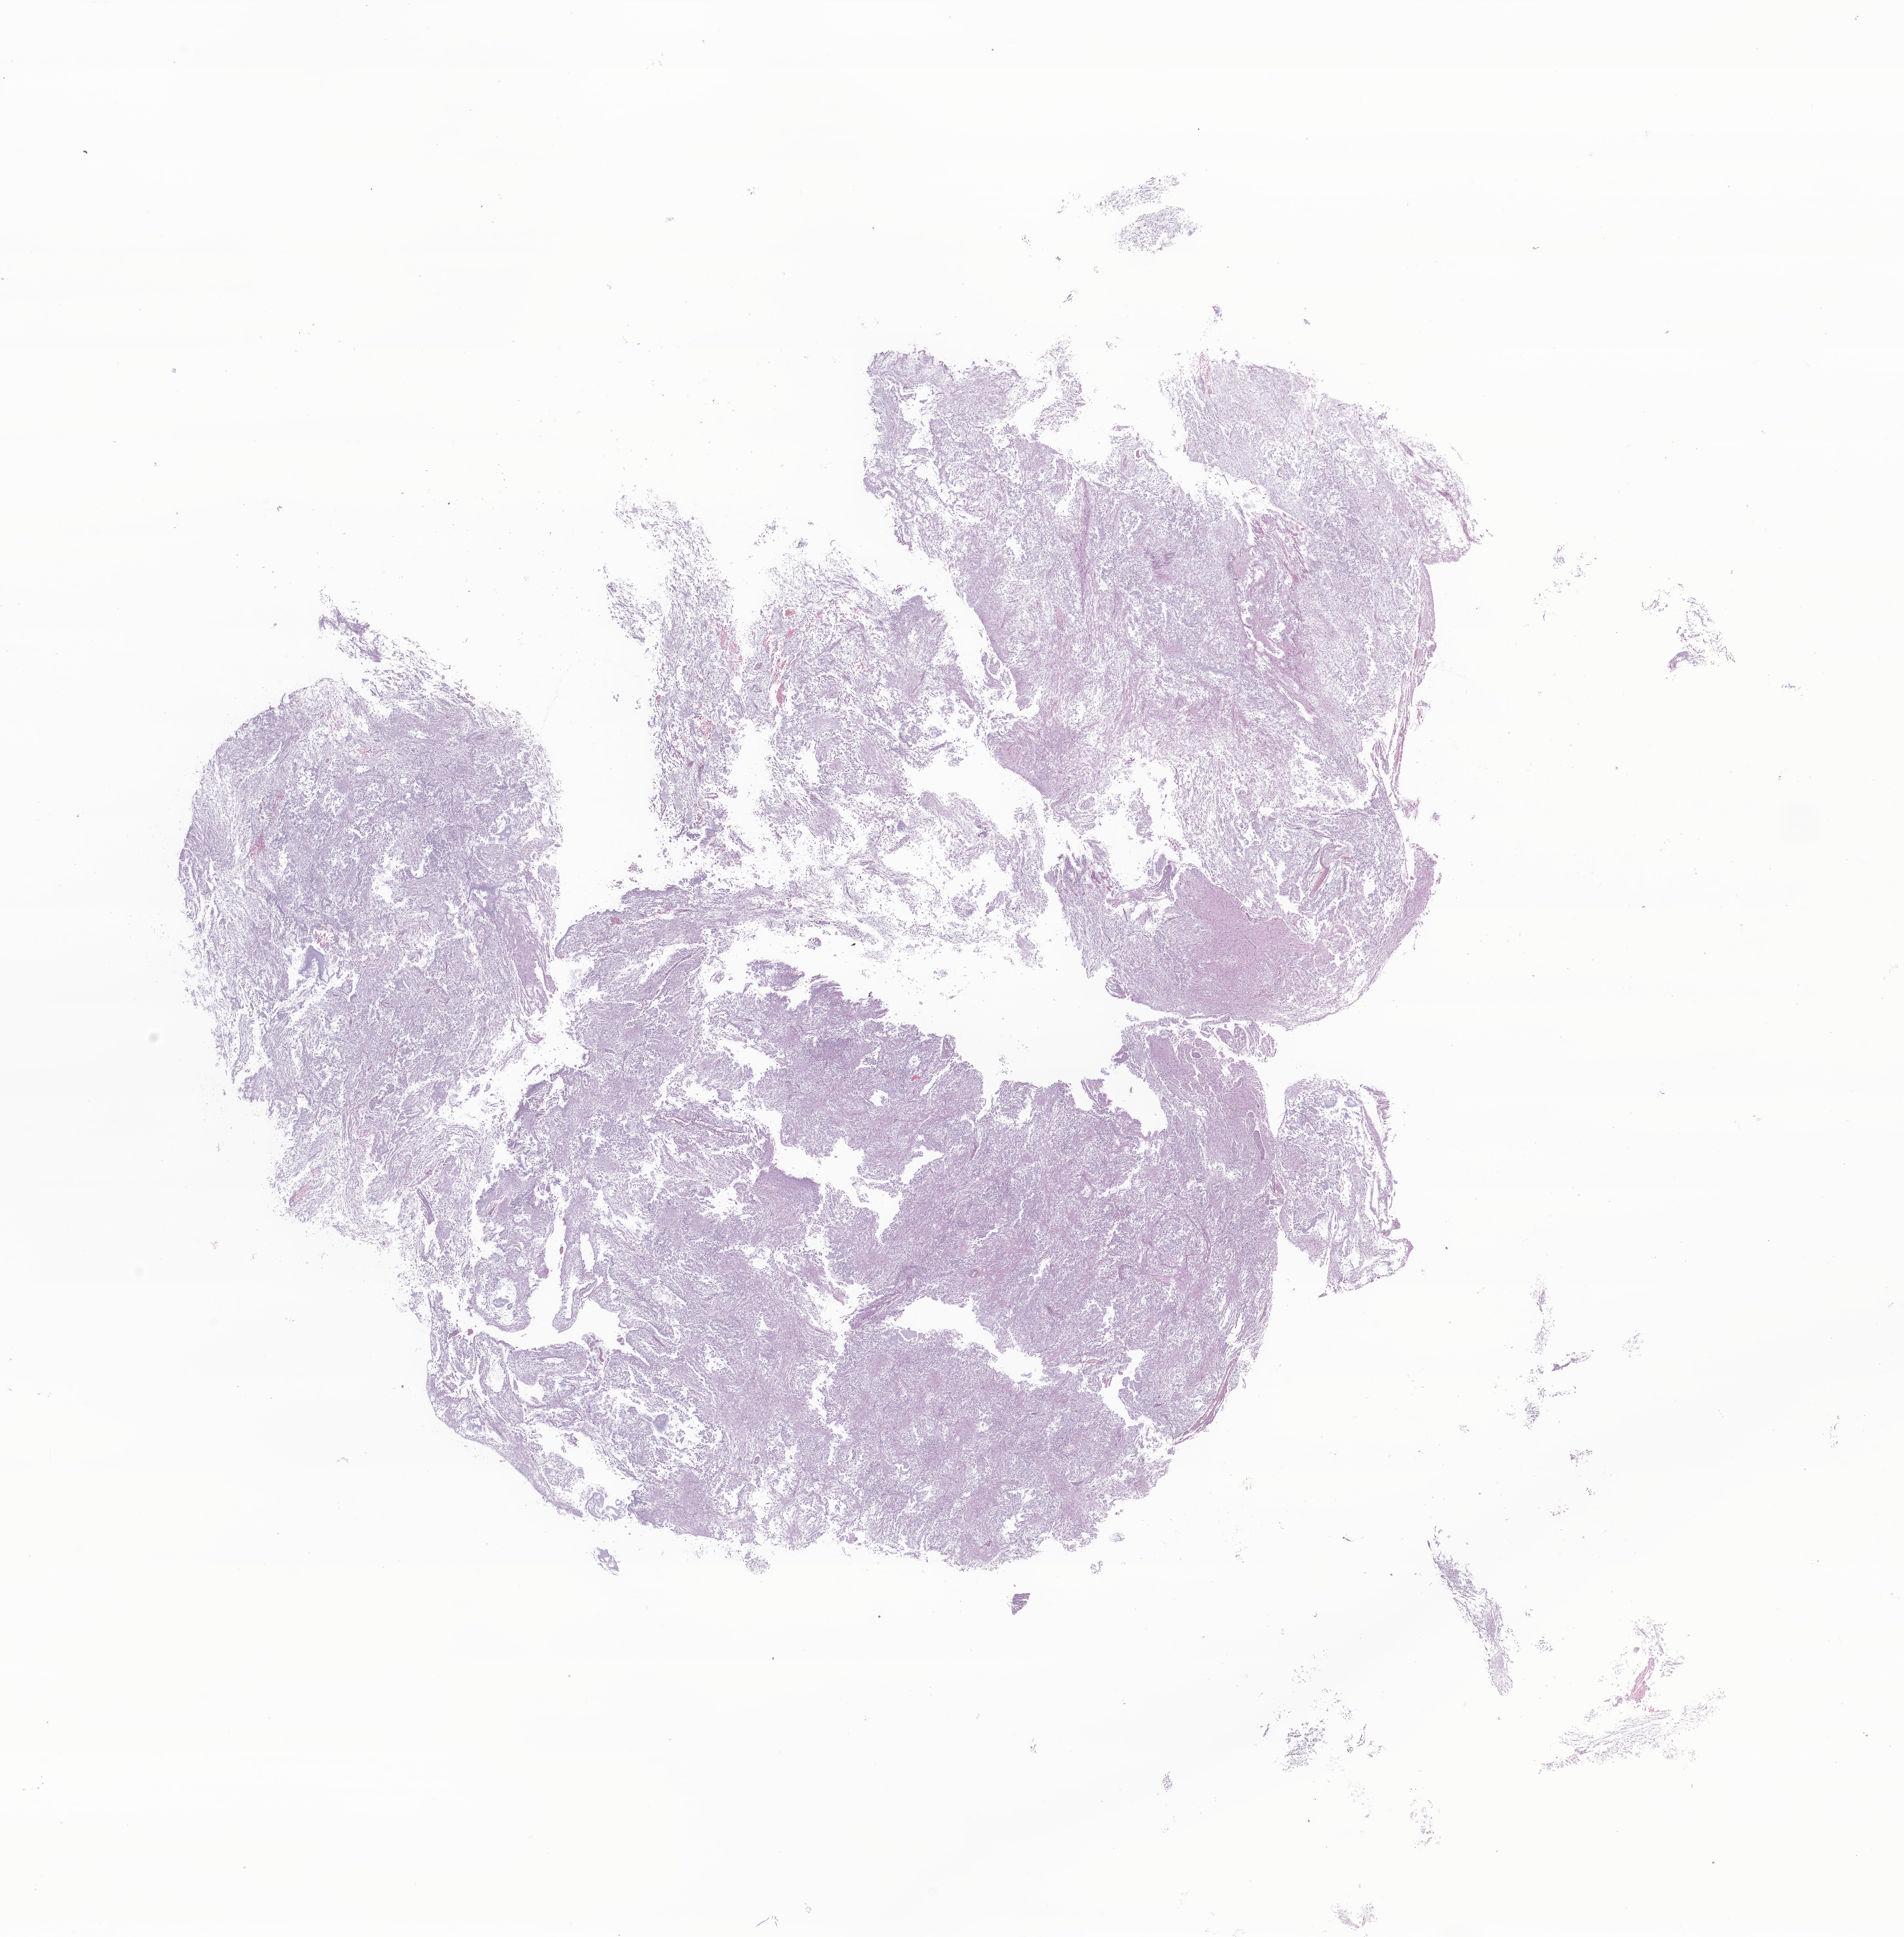
Whole-slide image, hematoxylin and eosin (H&E) stain of tumor tissue from the cerebellum — whole scanned area (about 21.7 x 22.1 mm) shown as a low-resolution overview. Formalin-fixed paraffin-embedded section. Female patient, age 91 months (7 years 7 months).
Recorded diagnosis: Tumor cells, uncertain whether benign or malignant.